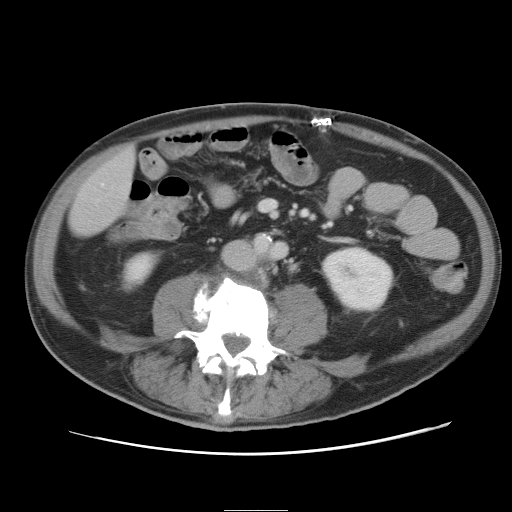
Contrast-enhanced abdominal CT, one axial slice; 120 kVp; intravenous contrast given; soft-tissue window (W 400 / L 40 HU); 512 × 512 image matrix, field of view 375 × 375 mm. Male patient, age 69 years. From the clinical record (not read from this slice): diagnosis: colorectal cancer liver metastases, imaged before liver resection; multiple liver metastases: no; largest metastasis: 8.5 cm; chemotherapy before resection: no.
Outlined on this slice (expert manual segmentation):
- liver: bounding box [x1, y1, x2, y2] px = [70, 149, 135, 237]
- planned liver remnant (the part of the liver to remain after resection): [70, 150, 135, 236]